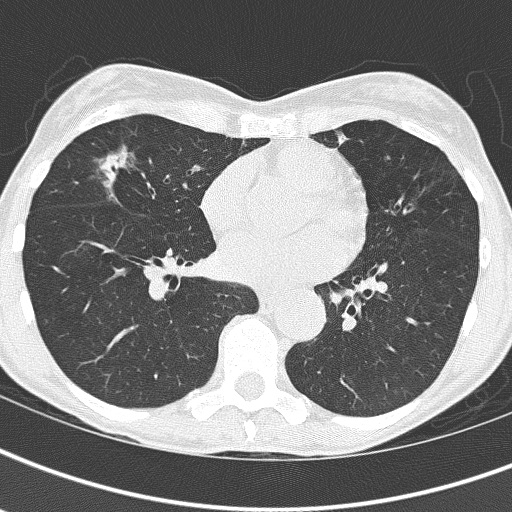
Axial slice from a low-dose chest CT screening exam; first (baseline) screen; lung window (W 1500 / L -600 HU); slice 94 of 161 in the series; 512 × 512 image matrix, field of view 290 × 290 mm. Female, age 67 years at enrolment. Current smoker at enrolment.
Expert-annotated lung lesion, bounding box <88,132,177,212> (left, top, right, bottom; pixels). No non-calcified nodule or mass ≥4 mm was recorded by the screening reader at this exam.